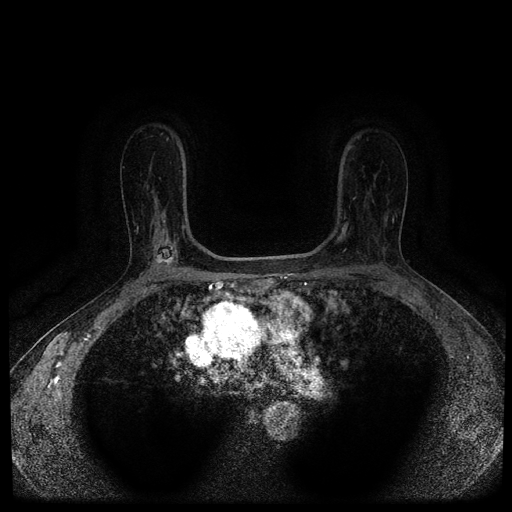
Breast MRI (dynamic contrast-enhanced, multi-phase), one axial slice; position 69 of 116 along the scan axis; dynamic contrast-enhanced series, time point 2 of 5 at this slice position (early post-contrast); 1.5 T; TE 2.7 ms, TR 5.4 ms; 2 mm slice thickness; 512 × 512 image matrix, field of view 330 × 330 mm. Patient: female, 63 years.
Annotated regions visible in this slice (semi-automatic segmentation, software-assisted and operator-edited):
- breast lesion (labelled 'tumour' in the annotation; benign lesions carry a separate 'benign' label): bounding box <154,240,178,268> (left, top, right, bottom; pixels)